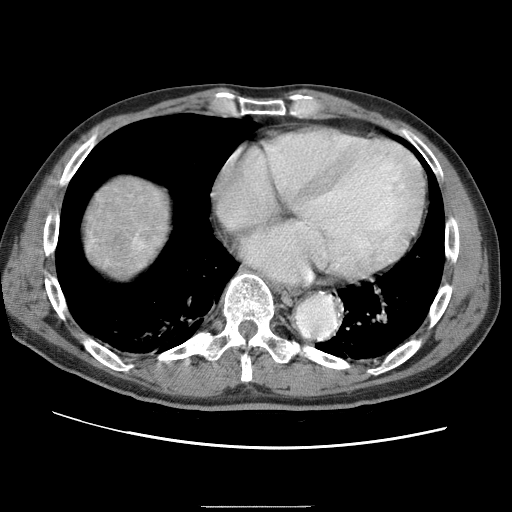
Contrast-enhanced abdominal CT (liver protocol), one axial slice. Slice 69 of 75 in the series (ordered by position). Reconstruction kernel STANDARD. One of 2 acquisitions stored at this slice position. Soft-tissue window (W 400 / L 40 HU). 2.5 mm slice thickness. 512 × 512 image matrix, field of view 360 × 360 mm. From the clinical record (not read from this slice): diagnosis: hepatocellular carcinoma (patient treated with transarterial chemoembolisation; whether this scan precedes or follows treatment is not stated here); TNM stage (as recorded): Stage-II; Child-Pugh class: A; tumour differentiation: well differentiated; tumour nodularity: multinodular.
Structures marked on this image (semi-automatically segmented with operator editing):
- liver parenchyma outside the tumour (the mass and vessels are separate outlines, so this box may not span the whole liver): bounding box (x1, y1, x2, y2) in pixels: (76, 166, 185, 286)
- mass: (78, 169, 161, 277)